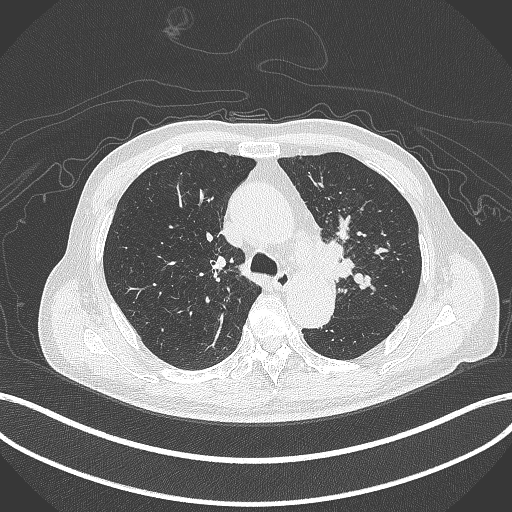
Chest CT, one axial slice; position 300 of 417 along the scan axis; reconstruction kernel B70f; 120 kVp; lung window (W 1500 / L -600 HU); 1 mm slice thickness; 512 × 512 image matrix, field of view 400 × 400 mm. Male patient, age 77 years. Case-level facts recorded for this patient, not image findings: clinical TNM (as recorded): T3 N1 M0.
Outlined on this slice (rectangle marked by the reading radiologist):
- lung tumour (recorded histology: adenocarcinoma): box from (x=314, y=235) to (x=356, y=283) px